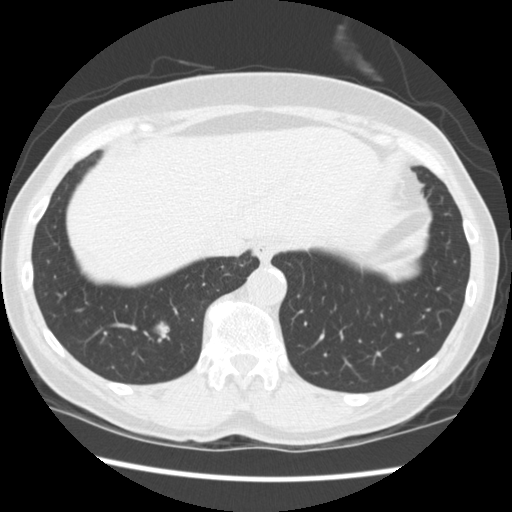
Low-dose screening chest CT, one axial slice. Slice 58 of 262 in the series (ordered by position). Reconstruction kernel STANDARD. Lung window (W 1500 / L -600 HU). 2.5 mm slice thickness. 512 × 512 image matrix, field of view 340 × 340 mm.
Annotated regions visible in this slice (expert manual segmentation):
- lesion 1 (tumor, lower lobe of right lung): bounding box <158,323,169,341> (left, top, right, bottom; pixels)